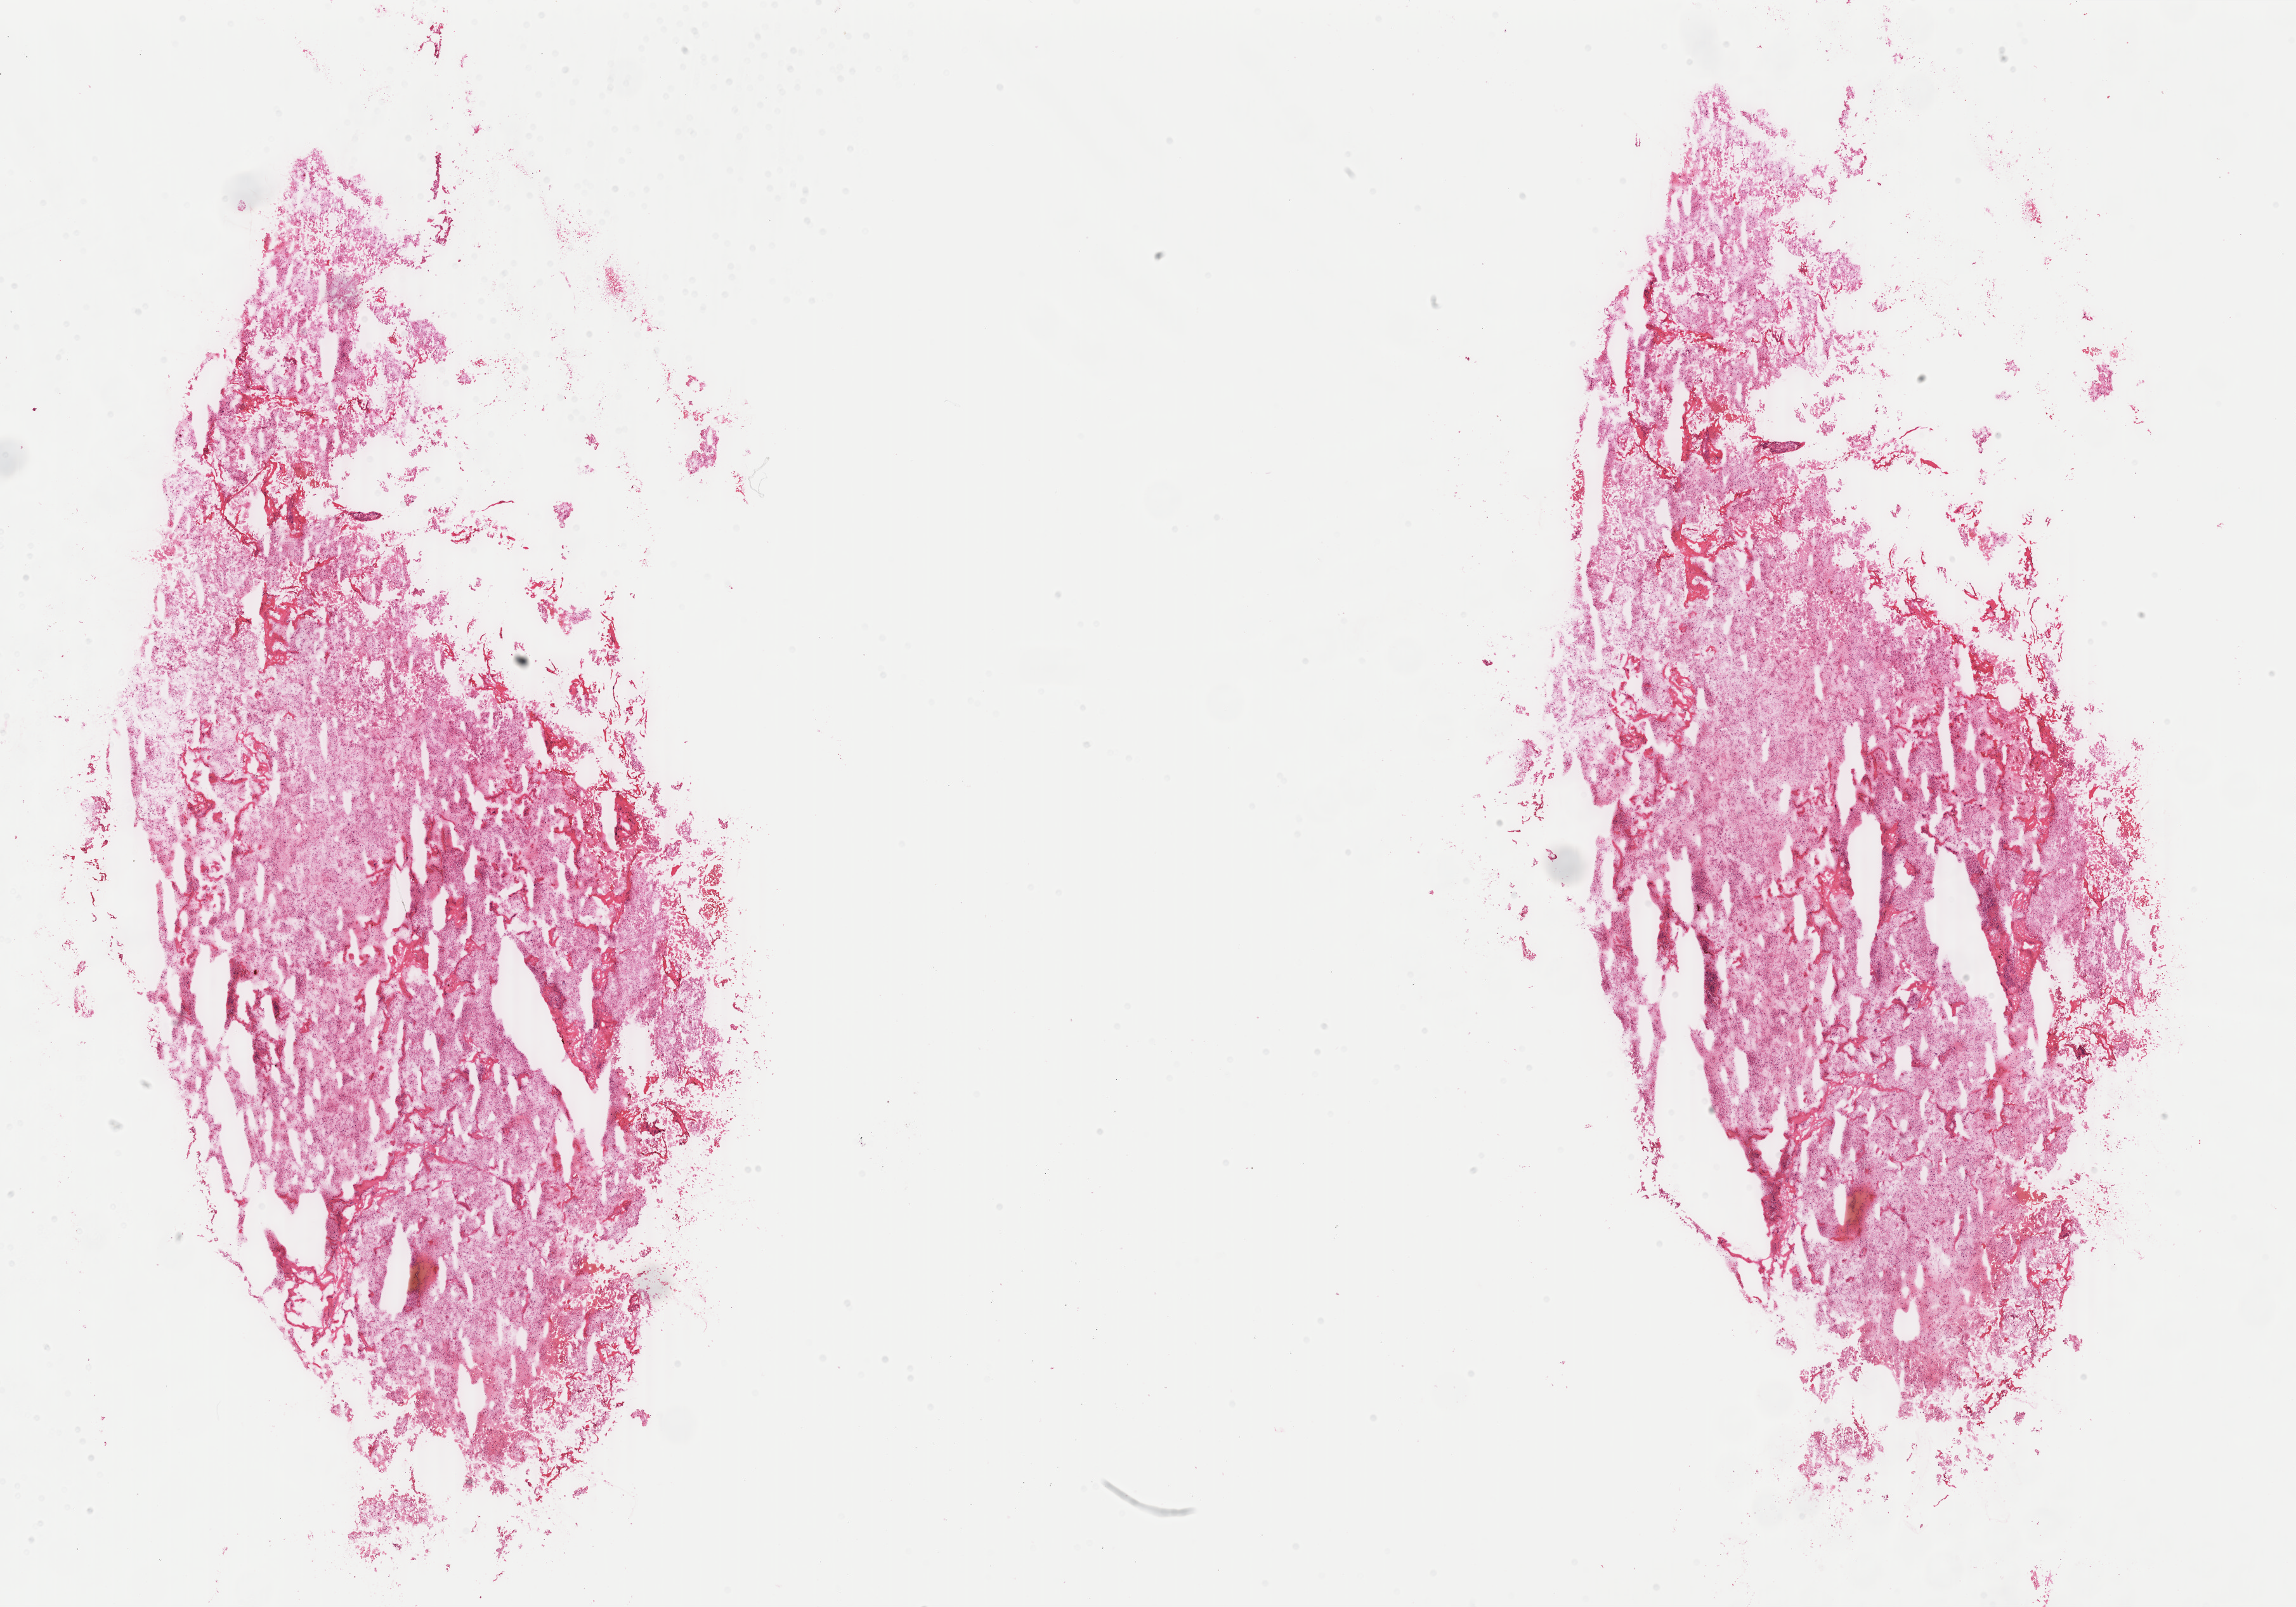
Whole-slide histology image, H&E — a low-resolution overview of the entire scanned area, about 28.8 x 20.1 mm. Frozen section from the top of the tissue portion. Primary tumour sample from the kidney. Patient: male, age at initial diagnosis 45 years.
Histologic diagnosis: Renal cell carcinoma, chromophobe type.